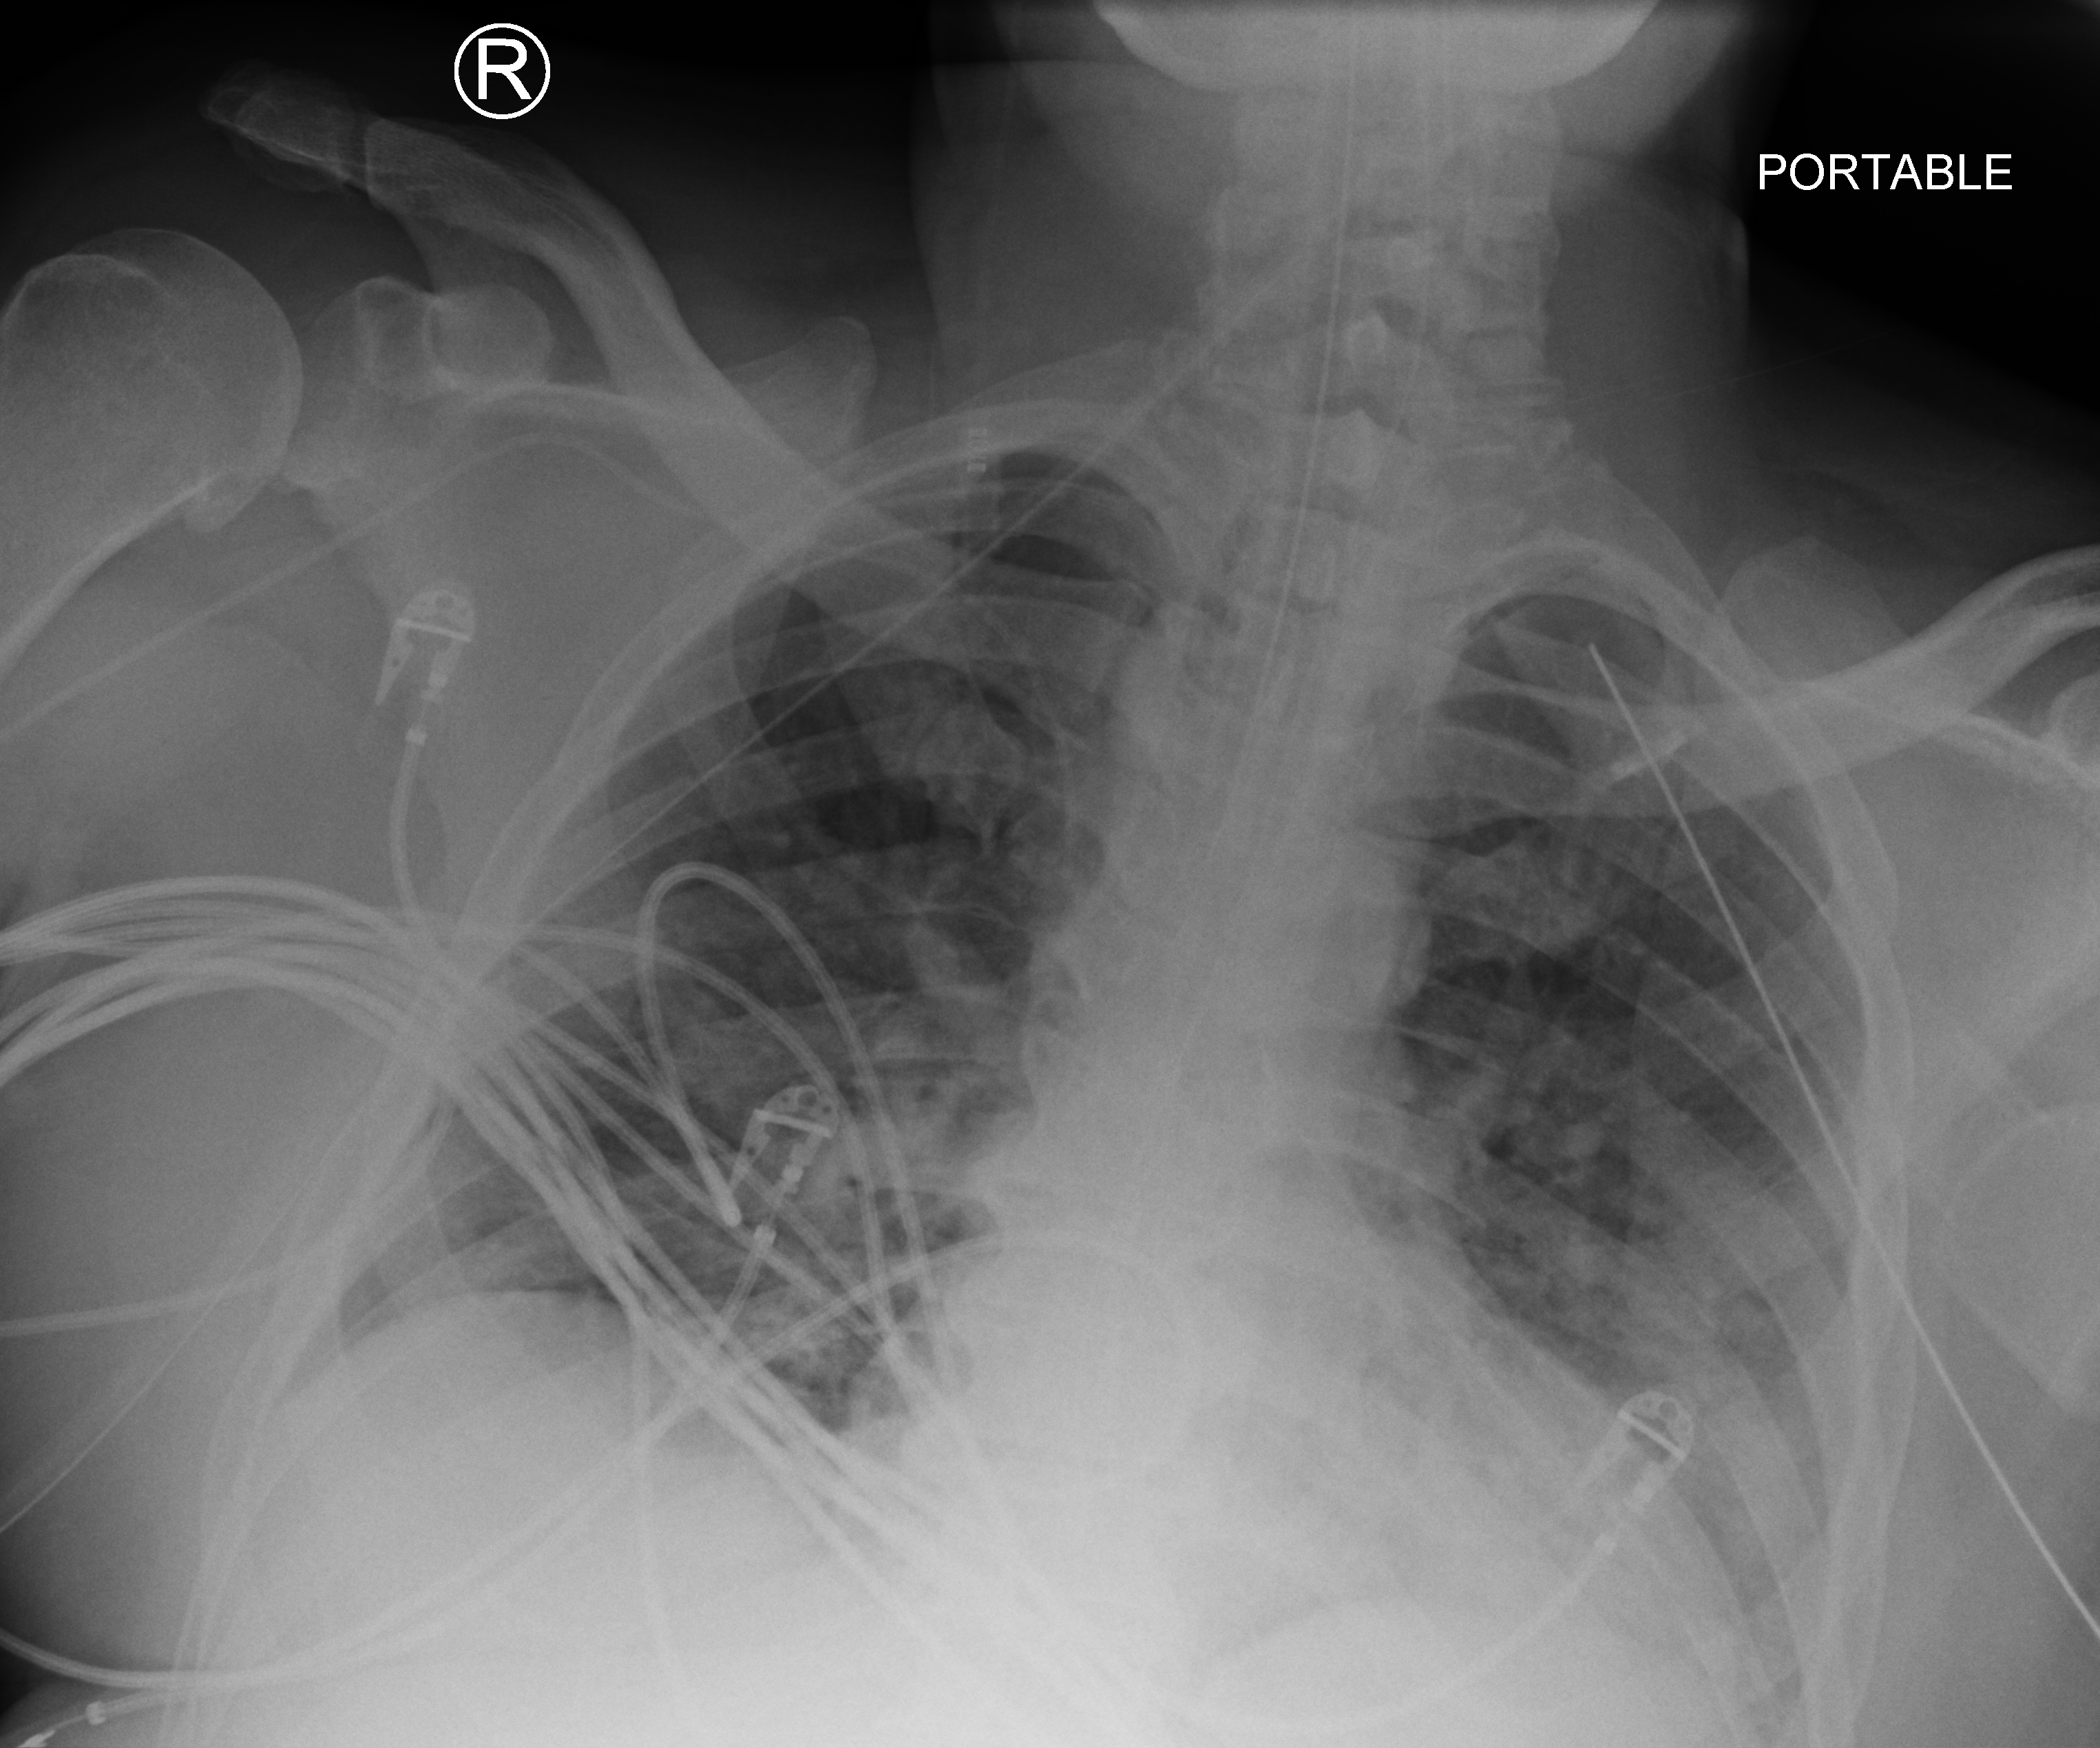
Portable chest radiograph; anteroposterior (AP) projection. Patient hospitalised with COVID-19; male, aged 18–59 years.
Admission-level facts for this patient (not findings on this image; timing relative to this image not recorded):
- length of hospital stay: 41 days